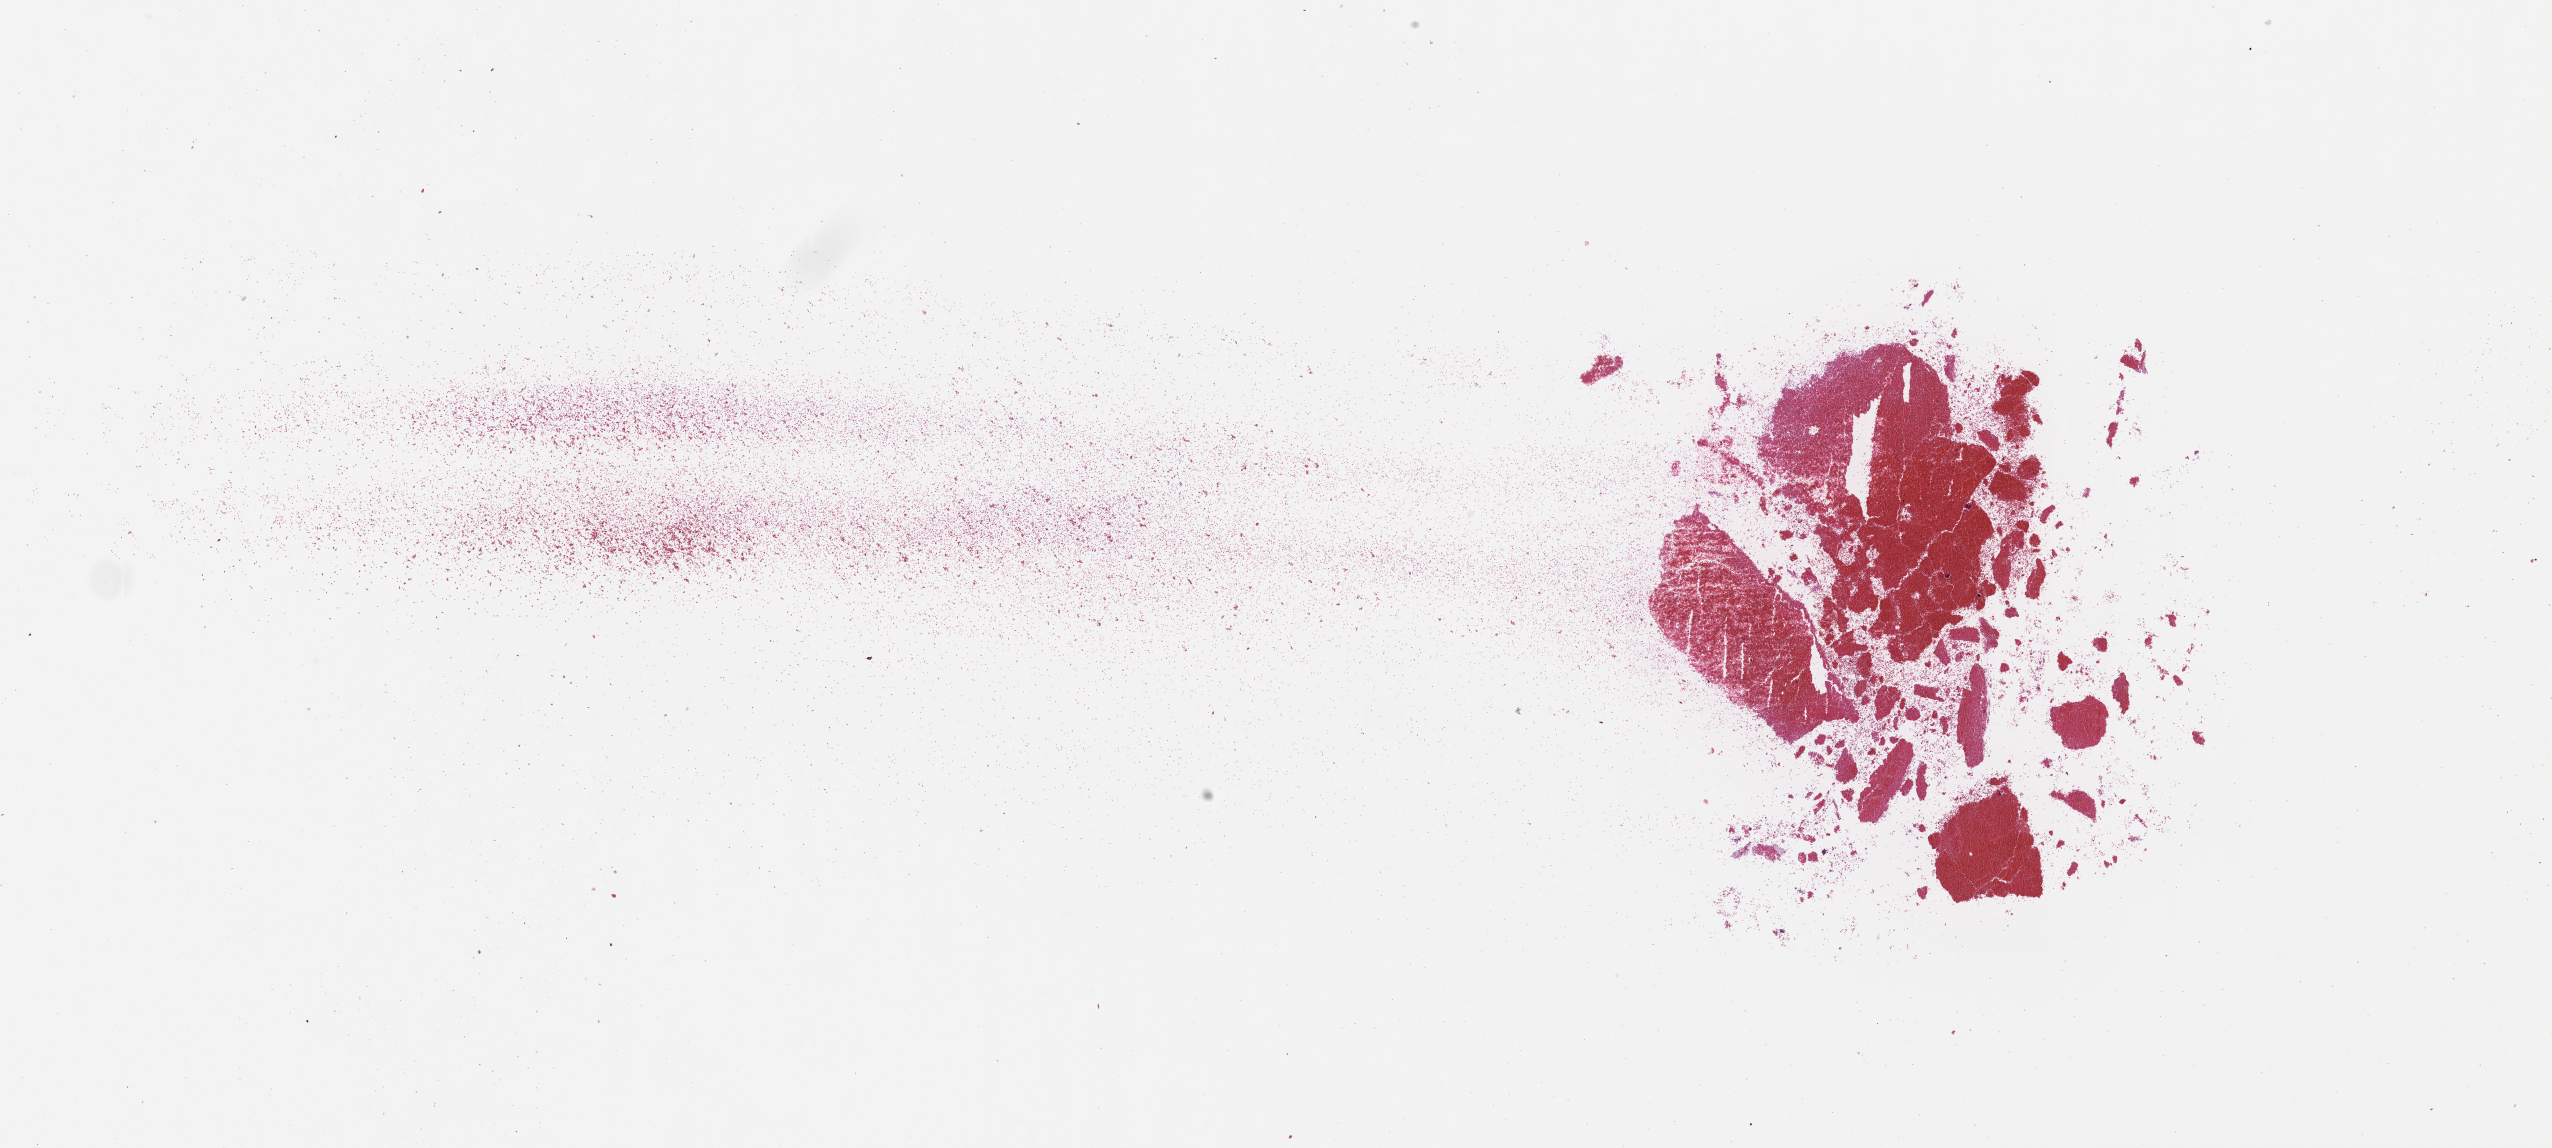
Haematoxylin and eosin whole-slide image — whole scanned area (about 20.6 x 9.3 mm) shown as a low-resolution overview. Formalin-fixed paraffin-embedded section. Archival tissue. Female patient.
This section: metastatic tumor tissue. Primary diagnosis of the patient: Colorectal Carcinoma.